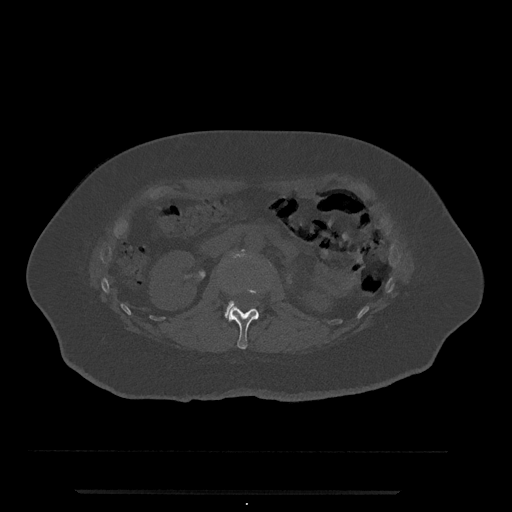
CT including the spine, one axial slice; slice 77 of 797 in the series (ordered by position); 120 kVp; bone window (W 1800 / L 400 HU); 0.5 mm slice thickness; 512 × 512 image matrix, field of view 440 × 440 mm. Patient: female, 51 years. Case-level facts recorded for this patient, not image findings: primary cancer: neuro.
Structures marked on this image (semi-automatically segmented with operator editing):
- L1 vertebra: box from (x=225, y=289) to (x=259, y=349) px
- L2 vertebra: (x=227, y=301)–(x=238, y=313)